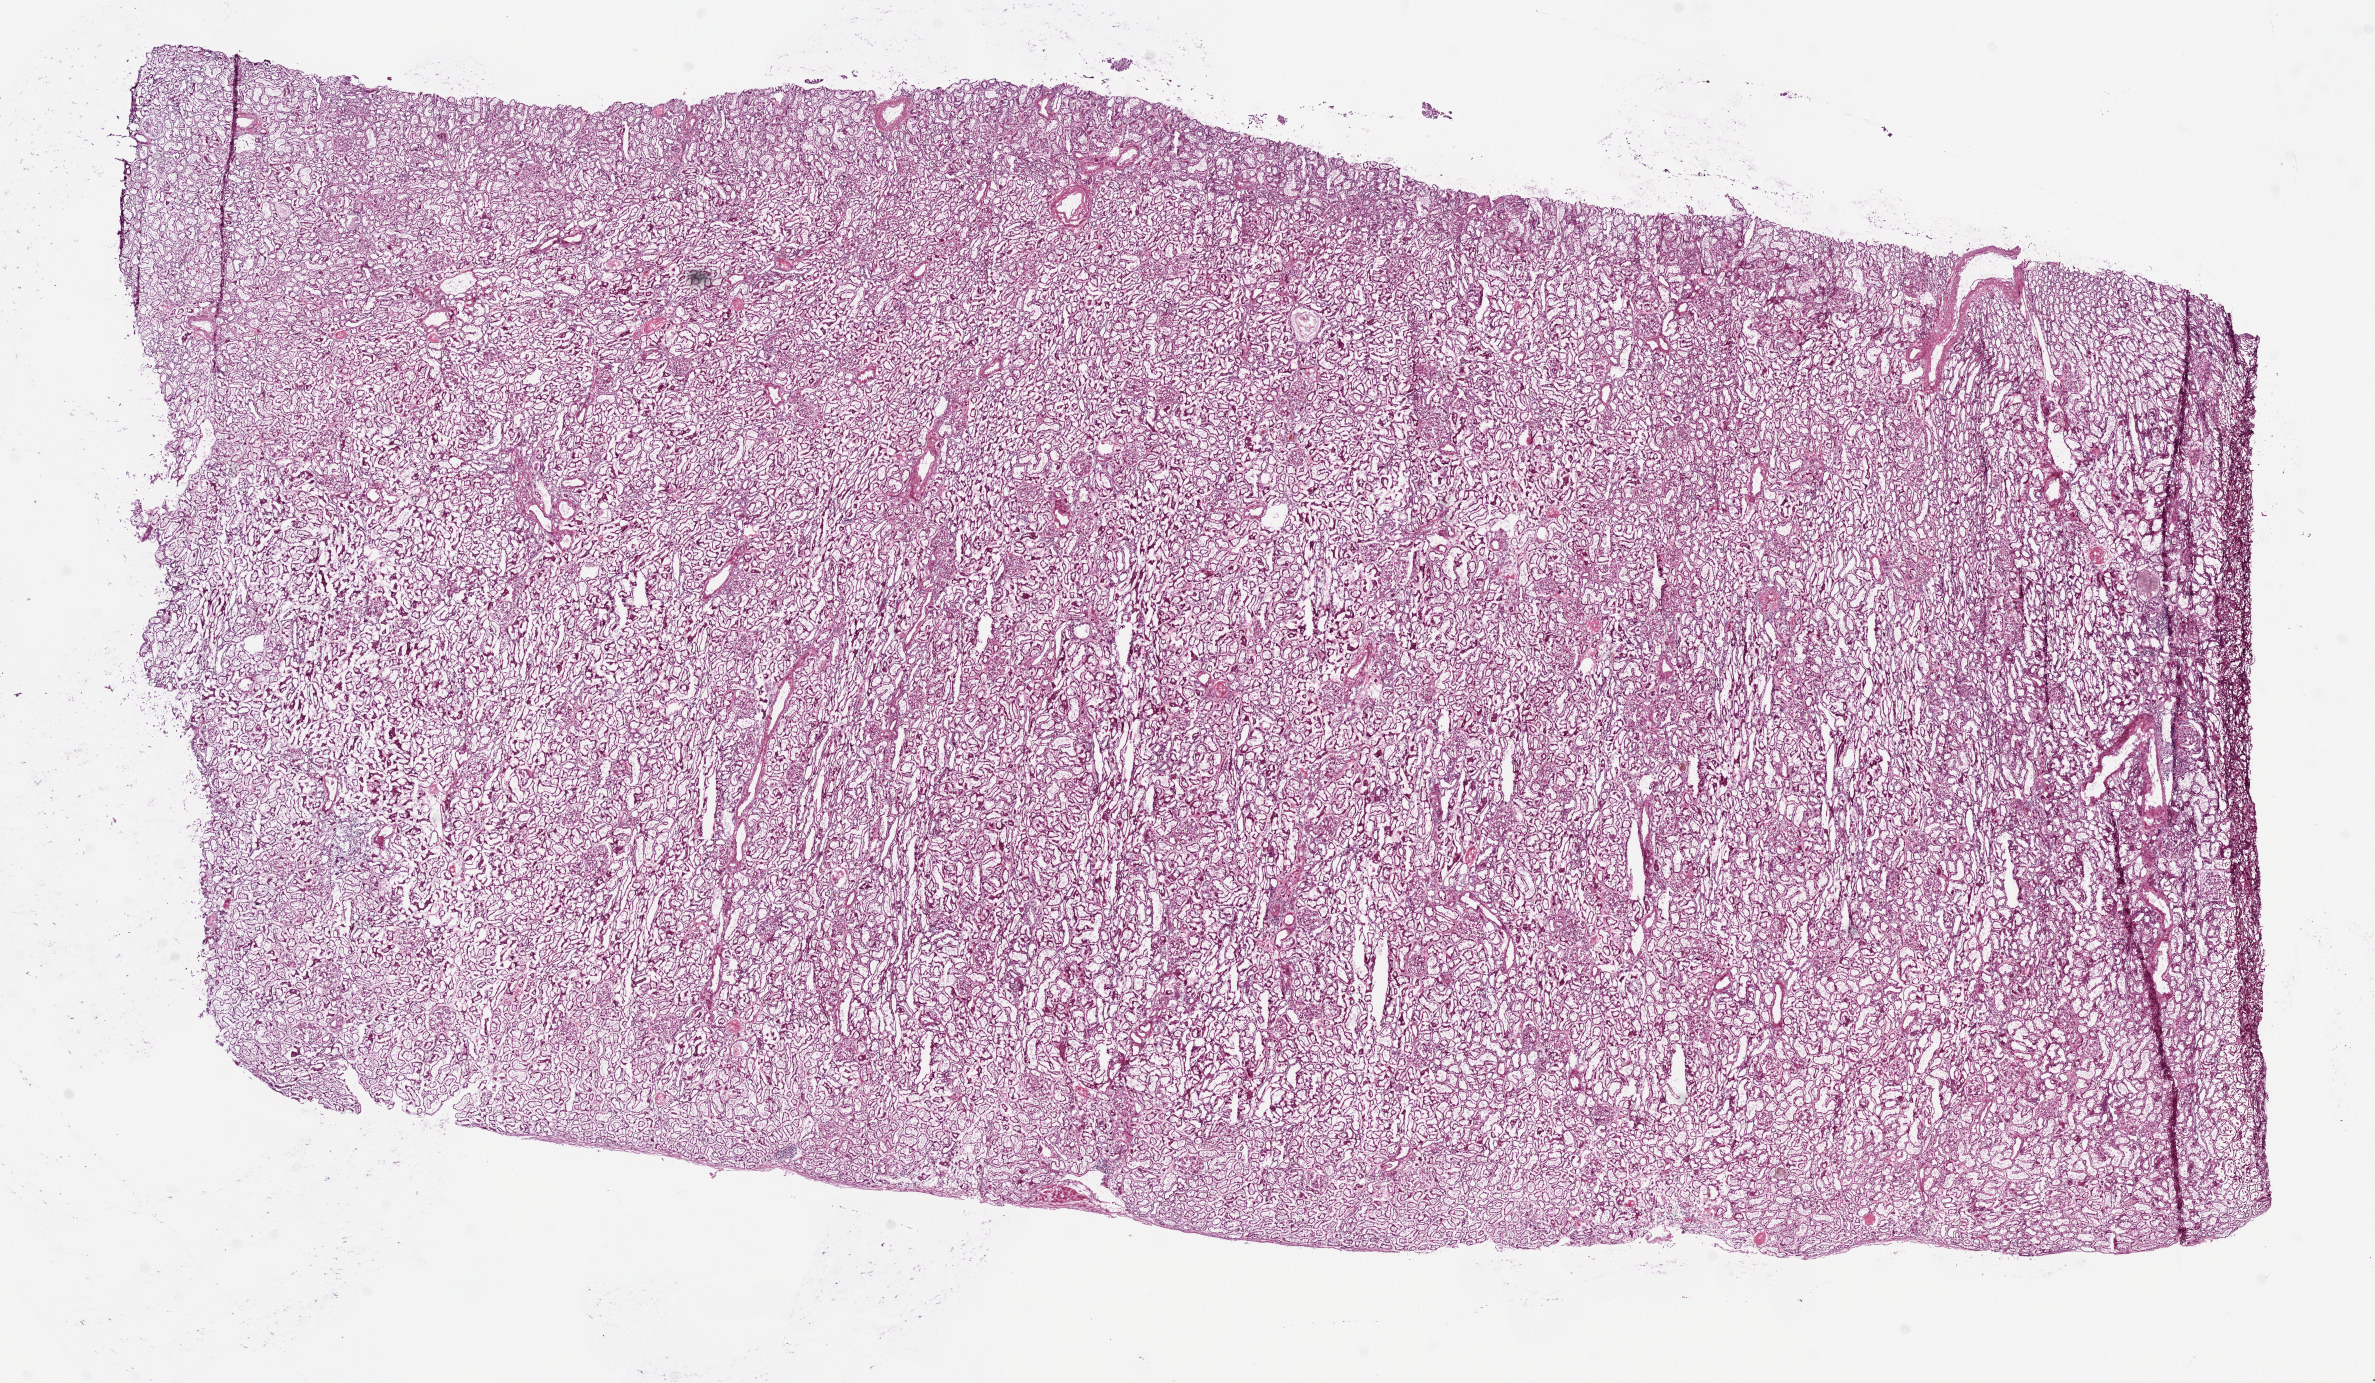
Whole-slide histology image, H&E — low-resolution overview of the scanned area, about 19.1 x 11.1 mm. Frozen section from the bottom of the tissue portion. Sample: solid tissue normal (non-tumour tissue), kidney. Female, age 78 years at initial diagnosis.
This section: solid tissue normal (non-tumour) sample from the same patient. Patient diagnosis: Clear cell adenocarcinoma, NOS.